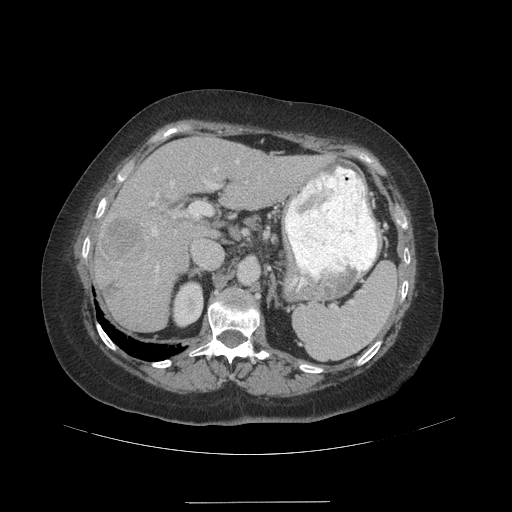
Contrast-enhanced abdominal CT (liver protocol), one axial slice. Slice 65 of 99 in the series (ordered by position). Soft-tissue window (W 400 / L 40 HU). 512 × 512 image matrix, field of view 440 × 440 mm. From the clinical record (not read from this slice): diagnosis: hepatocellular carcinoma (patient treated with transarterial chemoembolisation; whether this scan precedes or follows treatment is not stated here); TNM stage (as recorded): Stage-IVA.
Annotated regions visible in this slice (semi-automatically segmented with operator editing):
- liver parenchyma outside the tumour (the mass and vessels are separate outlines, so this box may not span the whole liver): bounding box [x1, y1, x2, y2] px = [94, 136, 328, 330]
- mass: [98, 216, 142, 296]
- liver vessels: [149, 160, 239, 273]